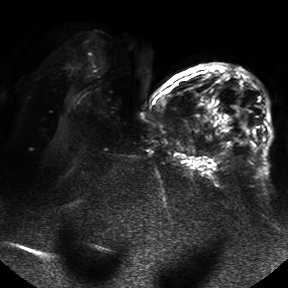
Breast MRI, one axial slice; slice 23 of 50 in the series (ordered by position); diffusion-weighted series; image 2 of 4 stored at this slice position (different b-values; order by instance number); 1.5 T; 288 × 288 image matrix, field of view 390 × 390 mm. Female patient.
Structures marked on this image (expert manual segmentation):
- tumour on diffusion-weighted imaging: bounding box (x1, y1, x2, y2) in pixels: (234, 106, 249, 133)